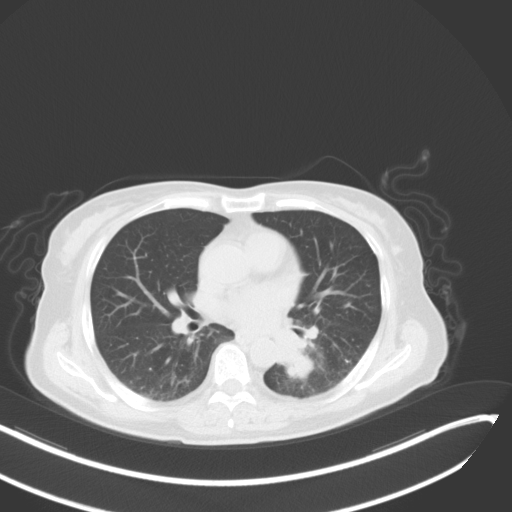
Chest CT, one axial slice; slice 19 of 48 in the series (ordered by position); reconstruction kernel B31f; lung window (W 1500 / L -600 HU); 5 mm slice thickness; 512 × 512 image matrix, field of view 400 × 400 mm. Patient: female, 64 years. From the clinical record (not read from this slice): clinical TNM (as recorded): T3 N1 M1; histopathological grade: G3.
Structures marked on this image (rectangle marked by the reading radiologist):
- lung tumour (recorded histology: small cell carcinoma): bounding box (x1, y1, x2, y2) in pixels: (271, 322, 317, 381)